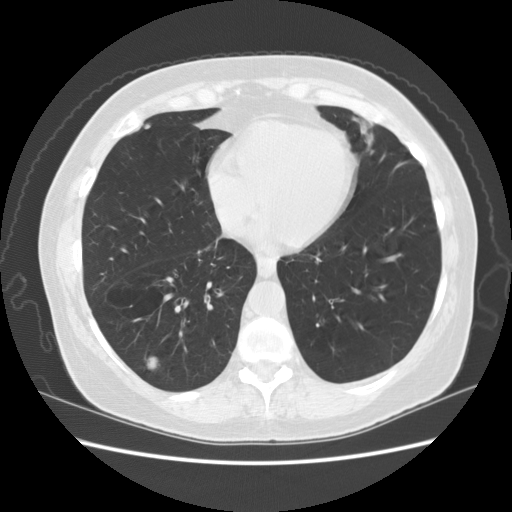
Axial slice from a low-dose chest CT screening exam; third screening round (two years after baseline); lung window (W 1500 / L -600 HU); 2.5 mm slice thickness. Female, age 59 years at enrolment. Current smoker at enrolment.
Expert reader's lesion annotation, bounding box [x1, y1, x2, y2] px = [134, 345, 171, 384]. Screening reader's record for this exam (one nodule recorded; not confirmed to be the boxed lesion): non-calcified nodule or mass ≥4 mm, right lower lobe, 16 × 11 mm, smooth margins, soft tissue attenuation, pre-existing on the prior screen: yes; interval growth: yes. Official screen result: positive, other. Participant outcome: lung cancer diagnosed 42 days after this screen — non-small cell carcinoma, right lower lobe, poorly differentiated (G3), stage IA (AJCC 6th edition), 15 mm at pathology.